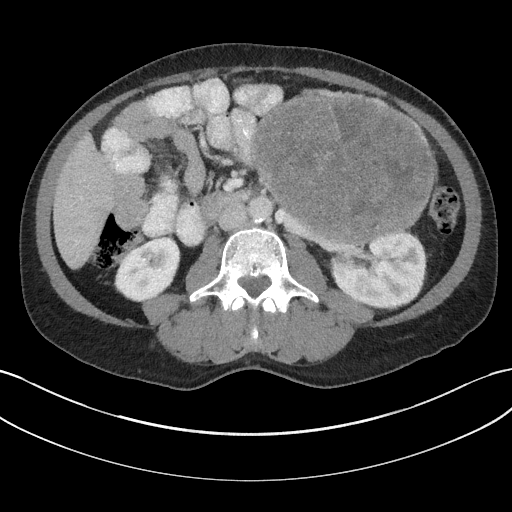
Contrast-enhanced abdominal CT, one axial slice. 100 kVp. Intravenous contrast given. Soft-tissue window (W 400 / L 40 HU). 512 × 512 image matrix, field of view 384 × 384 mm. Patient: male, 58 years. From the clinical record (not read from this slice): diagnosis: adrenocortical carcinoma; tumour side: left adrenal; tumour size at pathology: 22 cm; Ki-67 index: 26 %; stage (as recorded): 2.
Structures marked on this image (semi-automatic segmentation, software-assisted and operator-edited):
- mass: bounding box <252,97,433,240> (left, top, right, bottom; pixels)